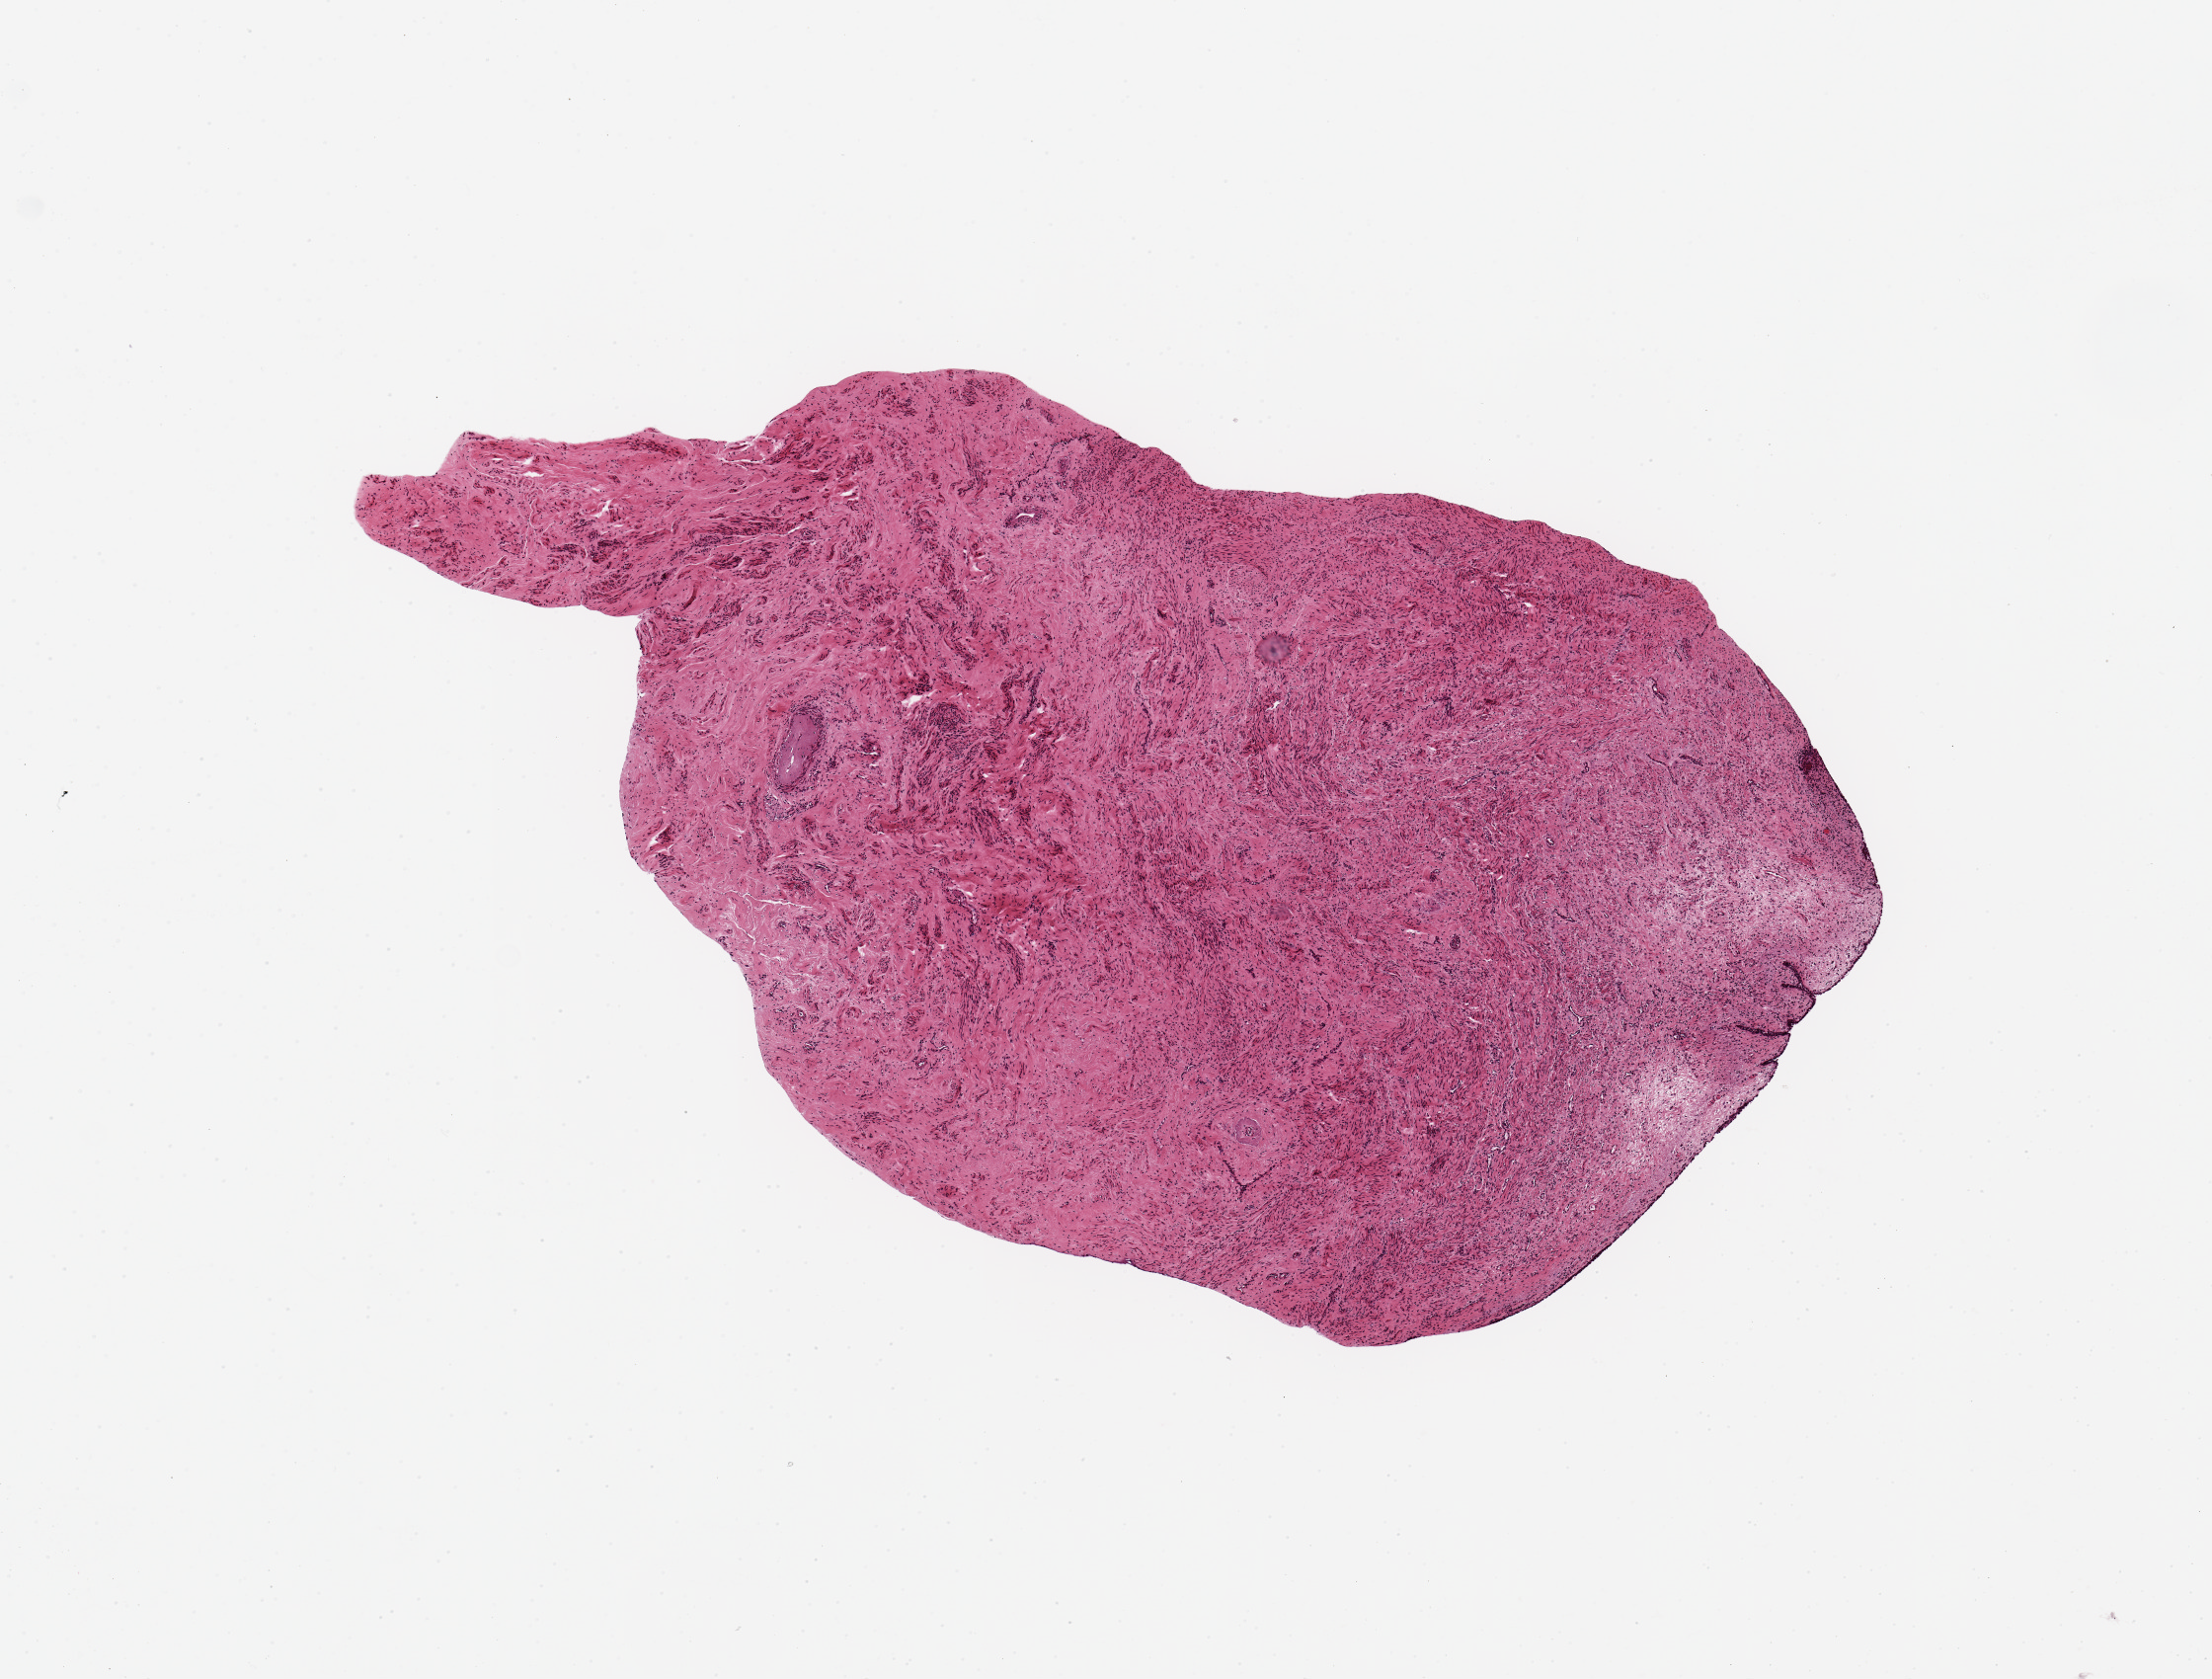
Whole-slide image, H&E stain — low-resolution overview of the scanned area, about 8.9 x 6.7 mm; PAXgene-fixed, paraffin-embedded tissue; section of exocervix (target tissue); donor tissue sample.
Review note (as recorded): 5 x 3.2mm. Essentially all stroma, single cell layer of degenerating epithelium along one edge.